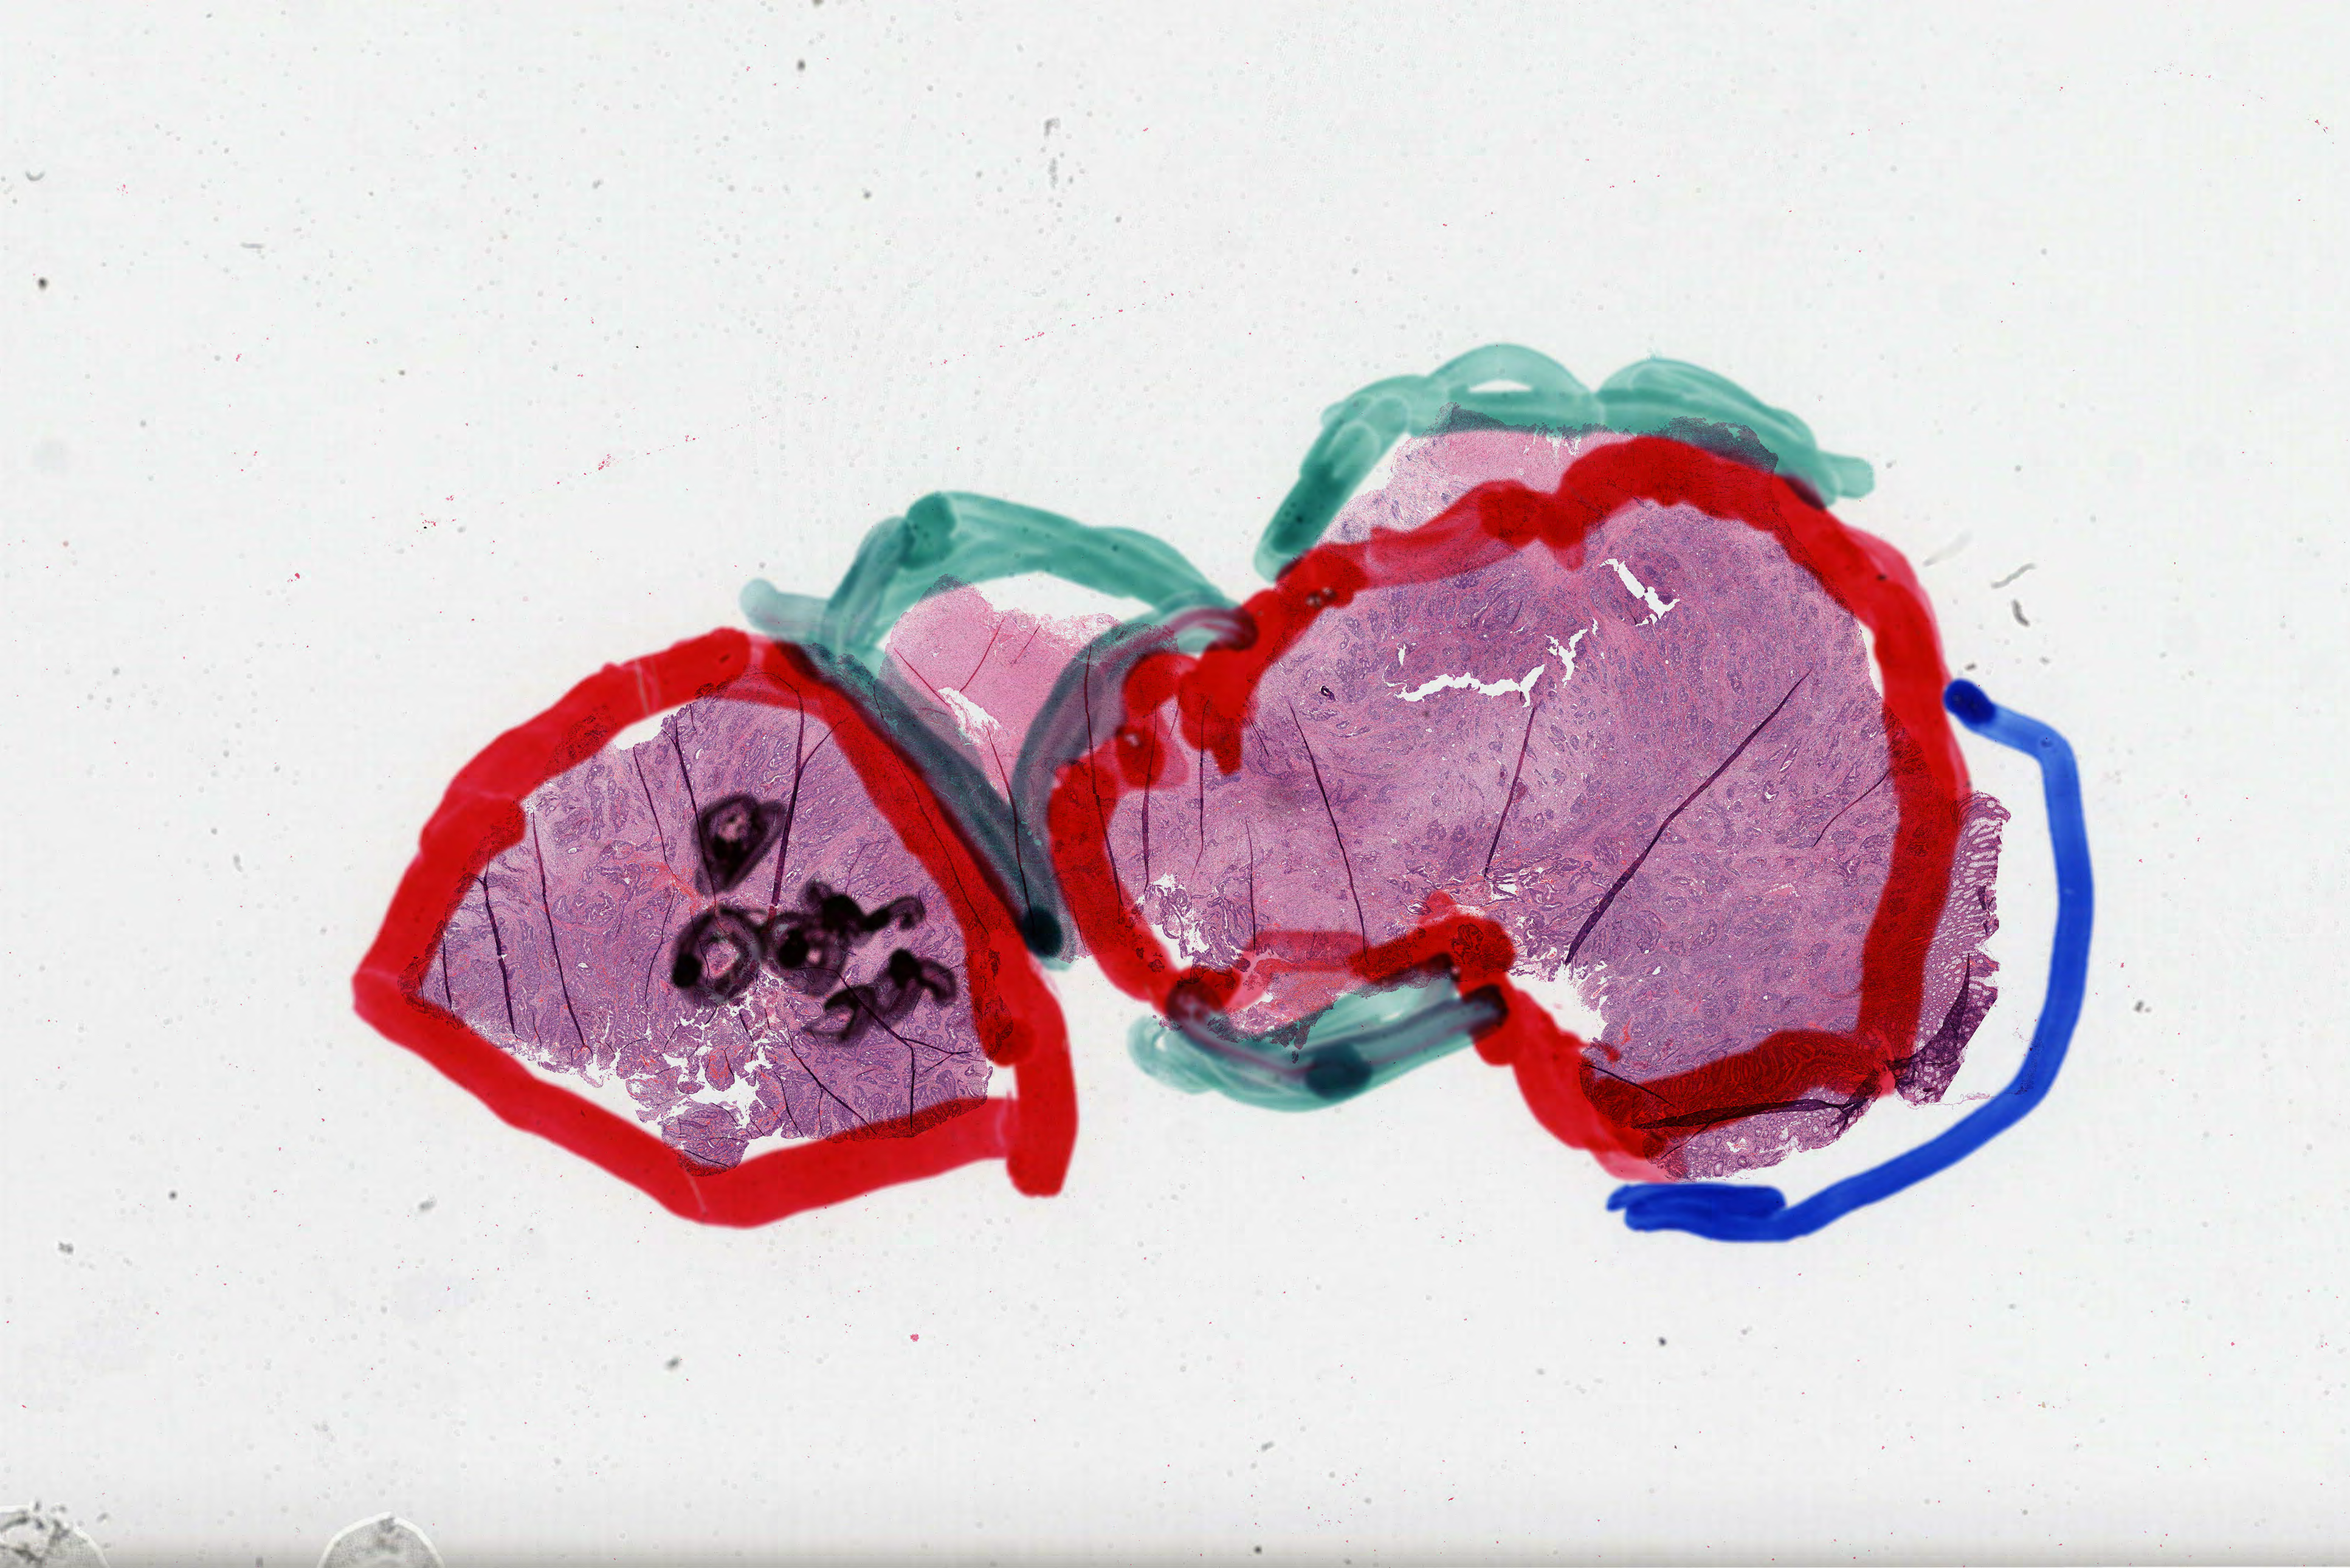
Hematoxylin and eosin (H&E) stained whole-slide image — low-resolution overview of the scanned area, about 31.2 x 20.8 mm (slide scanned at 40x). Formalin-fixed paraffin-embedded (FFPE) diagnostic section. Primary tumour sample from the rectum. Patient: male, age at initial diagnosis 71 years.
Lymph nodes positive (case pathology): 1 of 12 examined. Diagnosis: Adenocarcinoma, NOS. TNM: T3 N1 M1. AJCC pathologic stage: IVA.